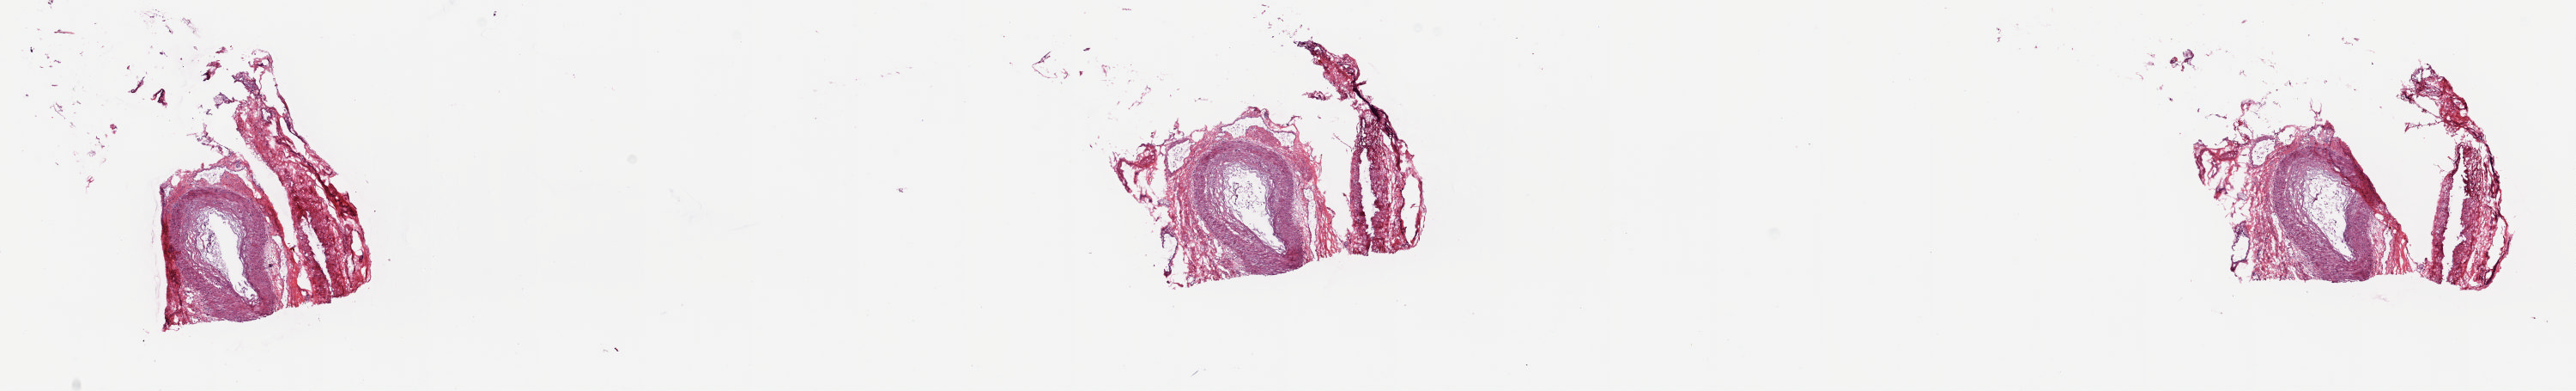
Digitized H&E-stained tissue section (whole slide) — shown as a low-resolution overview of the whole scanned area (about 23.8 x 3.6 mm, slide scanned at 20x), frozen section from the top of the tissue portion, sample: solid tissue normal (non-tumour tissue), prostate. Male patient; age at initial diagnosis 55 years. Pathologist review of this section (percent, as recorded): tumour cells 0%, tumour nuclei 0%, normal cells 100%, stromal cells 0%, necrosis 0%. Infiltration values recorded for this section: lymphocyte infiltration 5%, monocyte infiltration 0%, neutrophil infiltration 0%.
This section: solid tissue normal sample (biorepository sample class). Patient diagnosis: Adenocarcinoma, NOS (prostate gland).